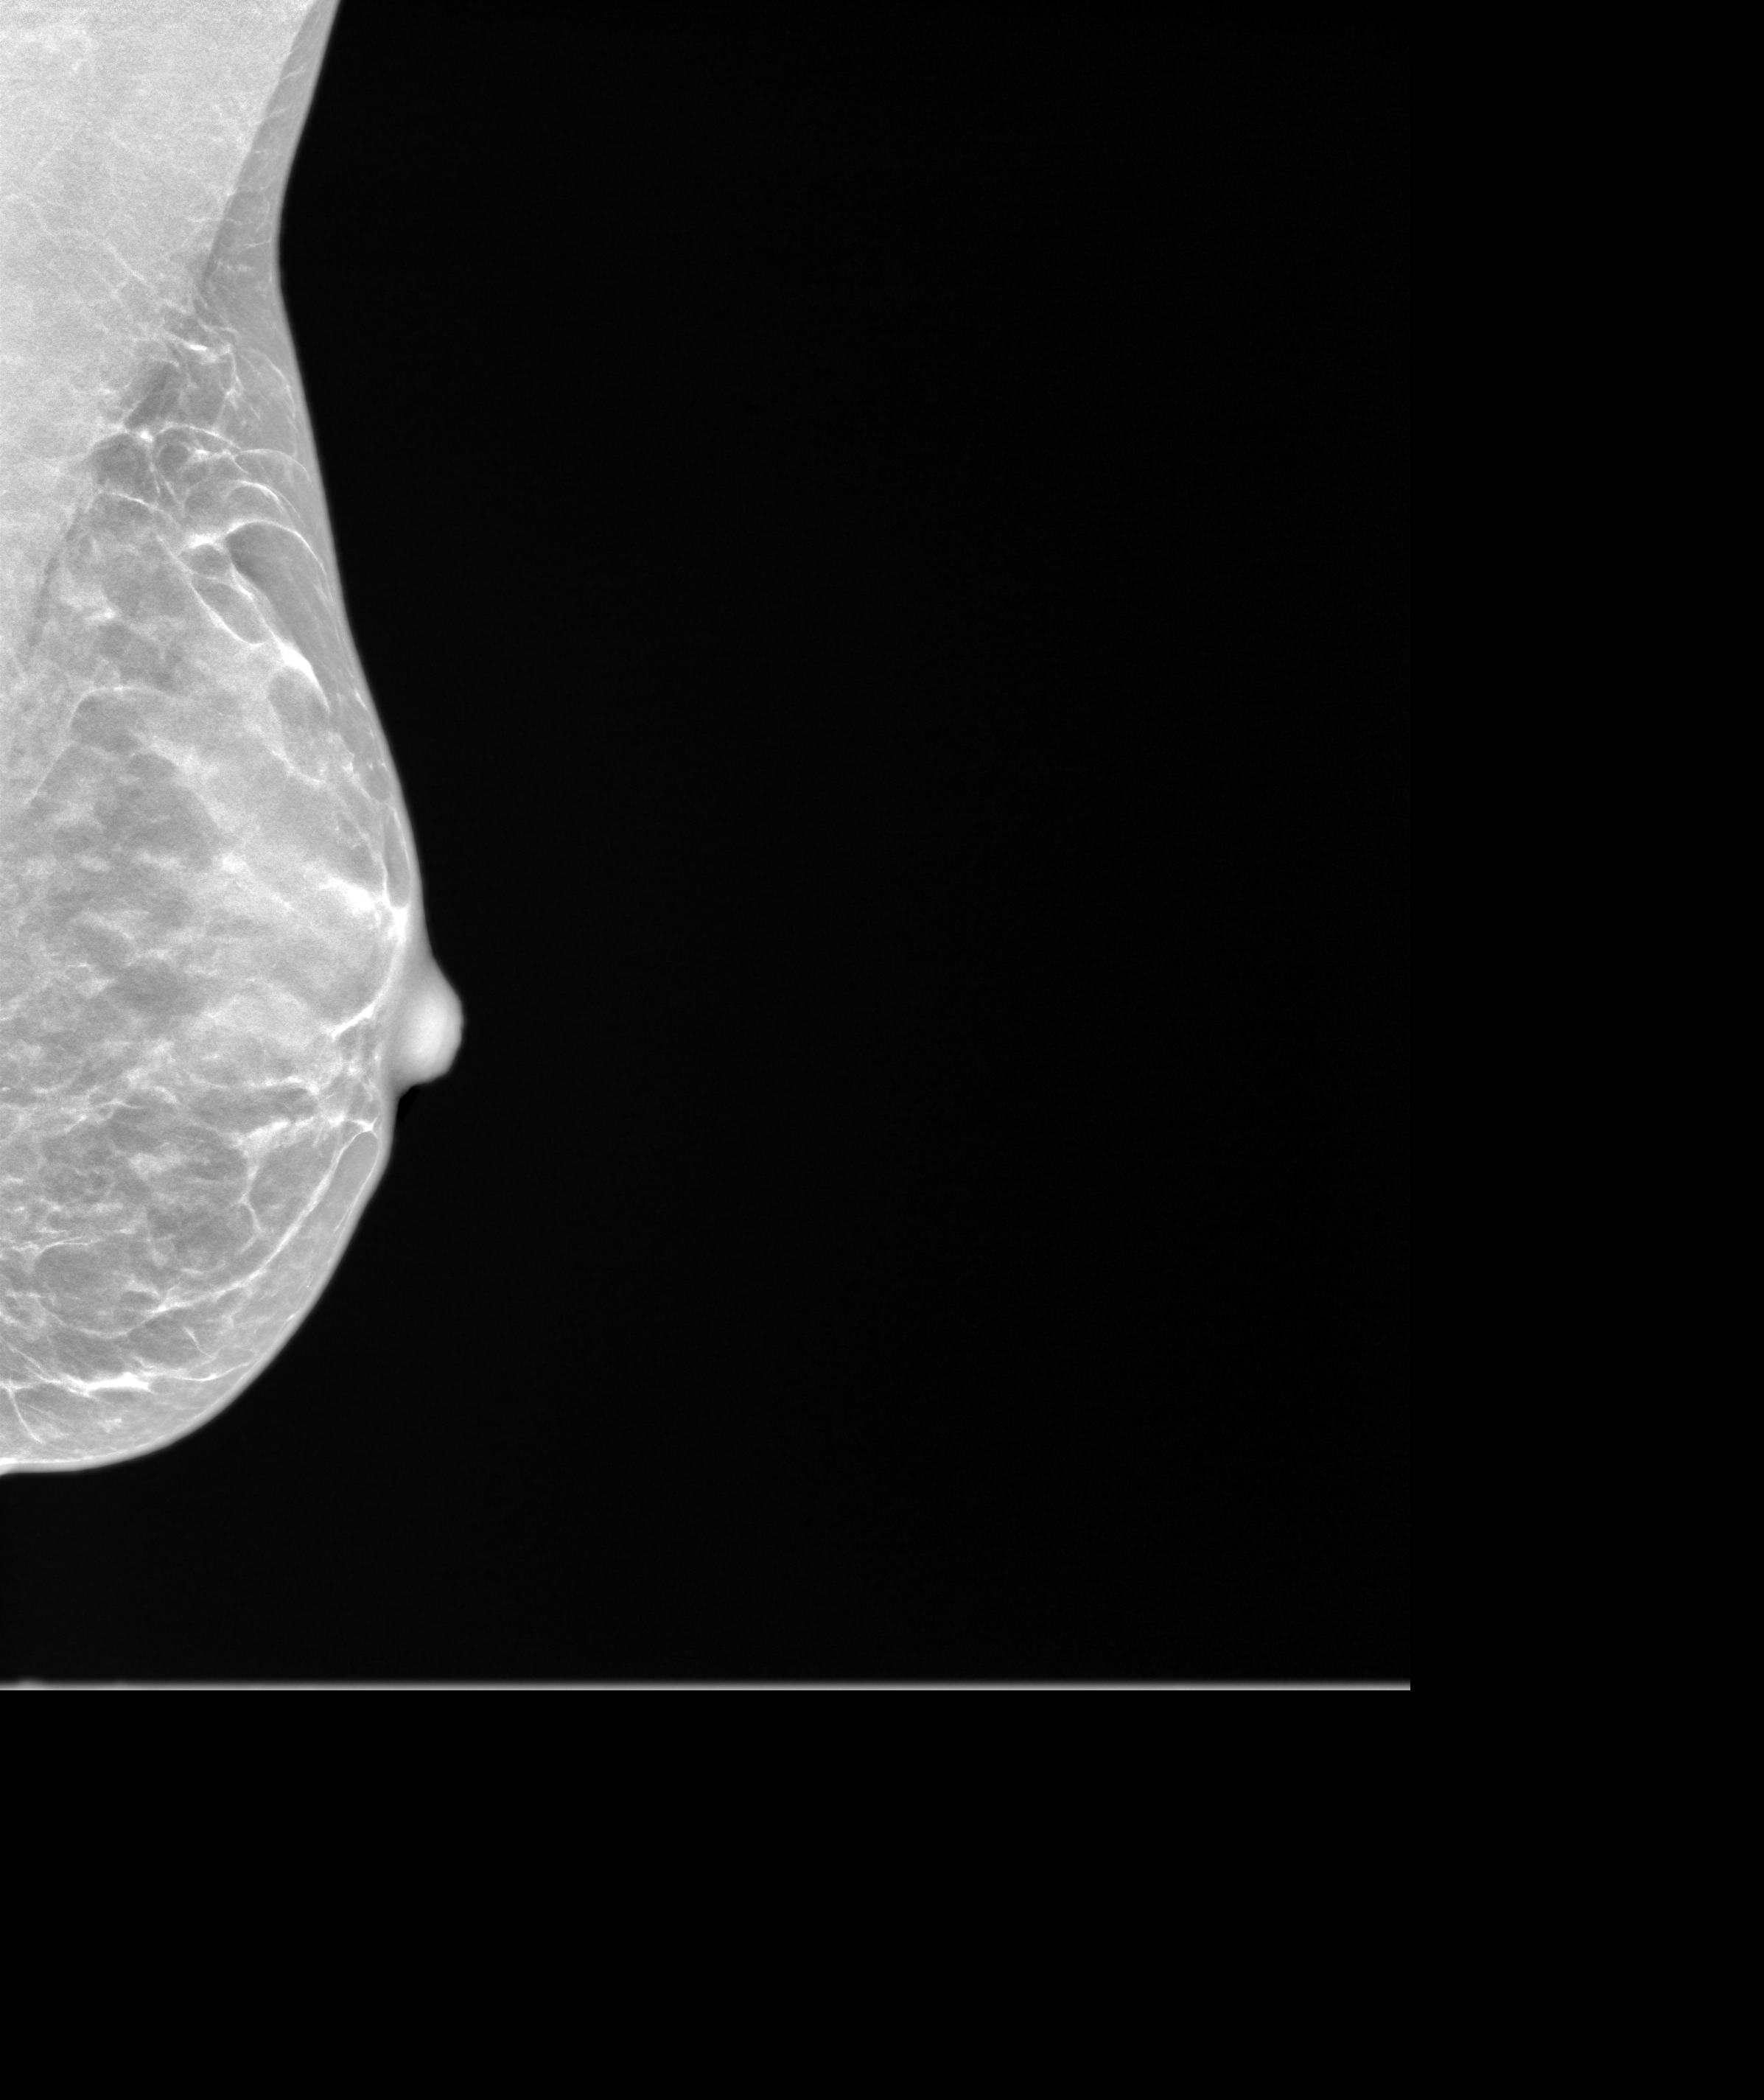
Screening examination; system: SenoIris_1SP1.1(421). Female patient, age 55 years.
Image type: synthesized 2-D view from tomosynthesis. Breast: left. Projection: mediolateral oblique (MLO) view.